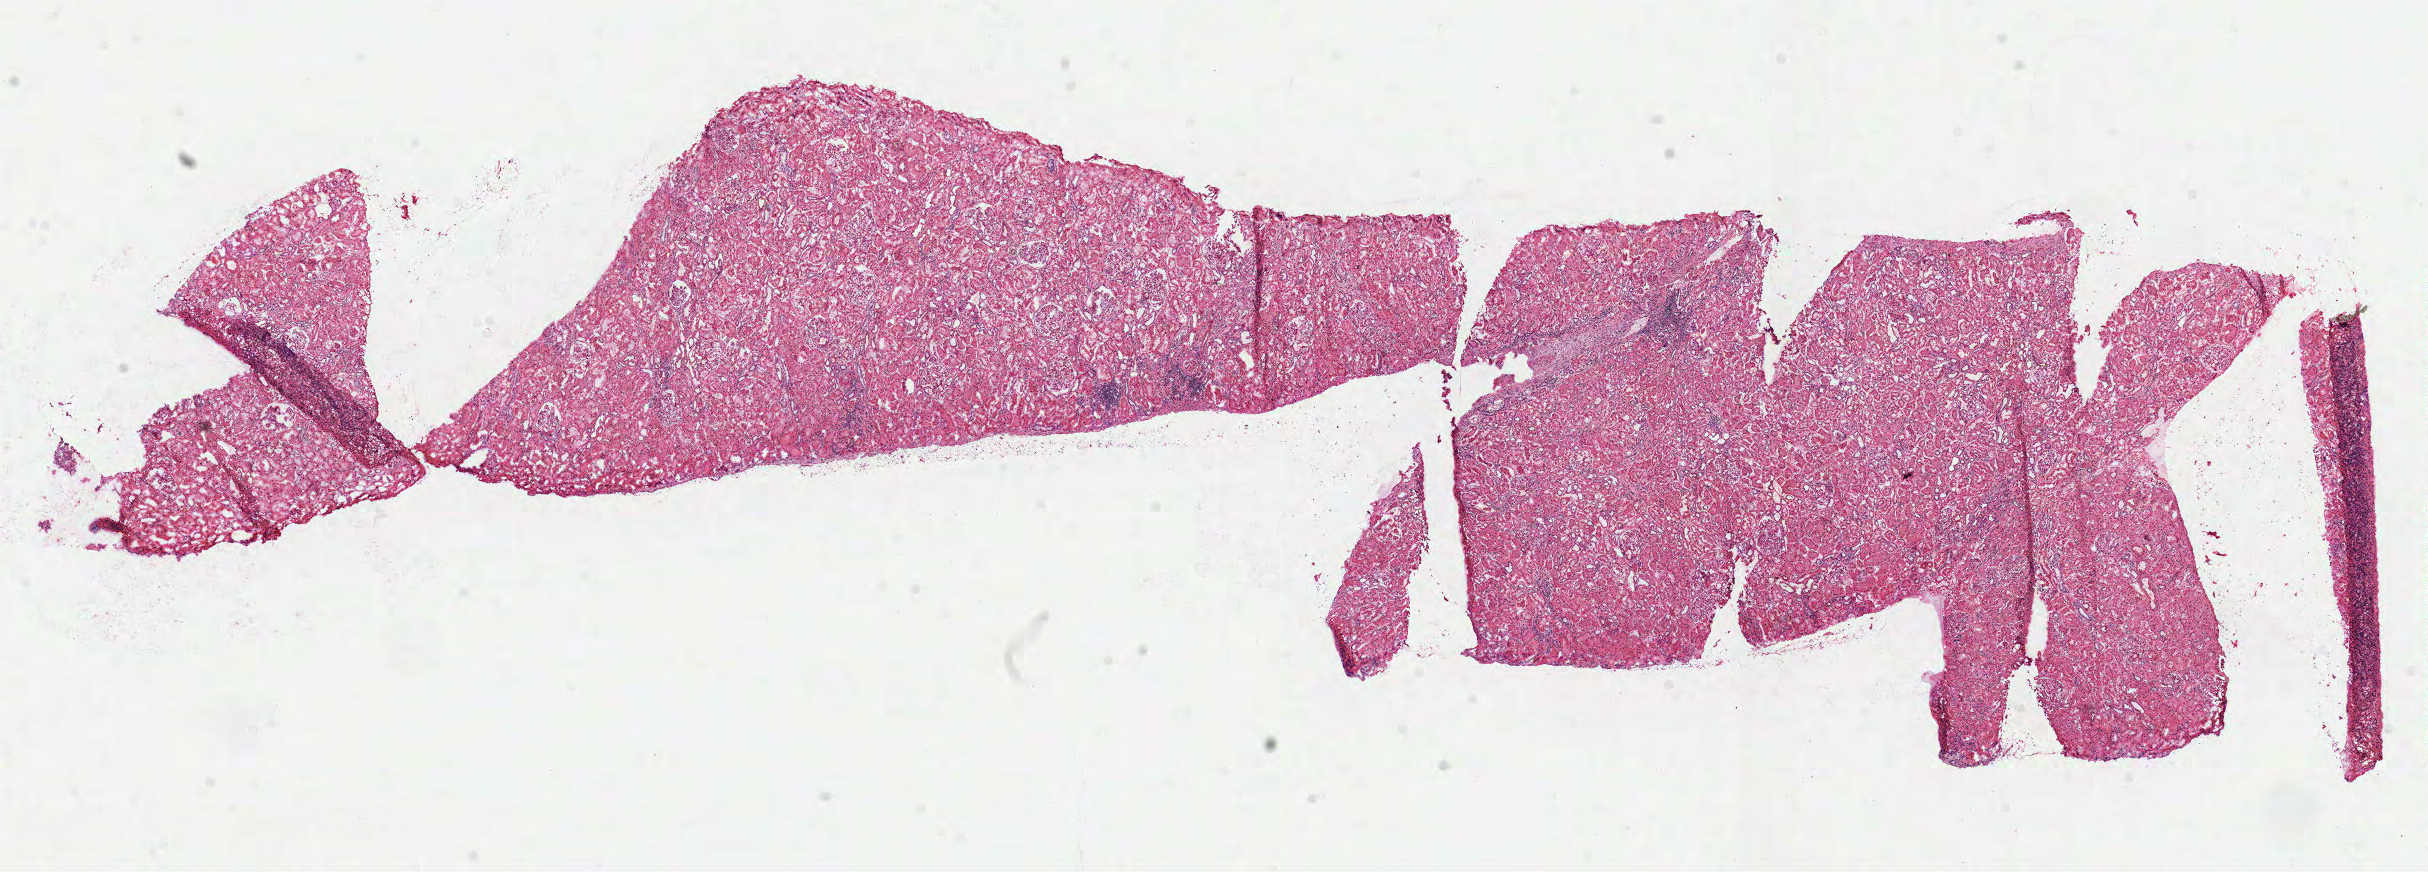
Digitized H&E tissue section (whole slide) — shown as a low-resolution overview of the whole scanned area (about 19.6 x 7.0 mm). Frozen section from the top of the tissue portion. Solid tissue normal (non-tumour tissue) sample from the kidney. Male patient; age at initial diagnosis 58 years.
This section: solid tissue normal sample (biorepository sample class). Patient diagnosis: Clear cell adenocarcinoma, NOS.